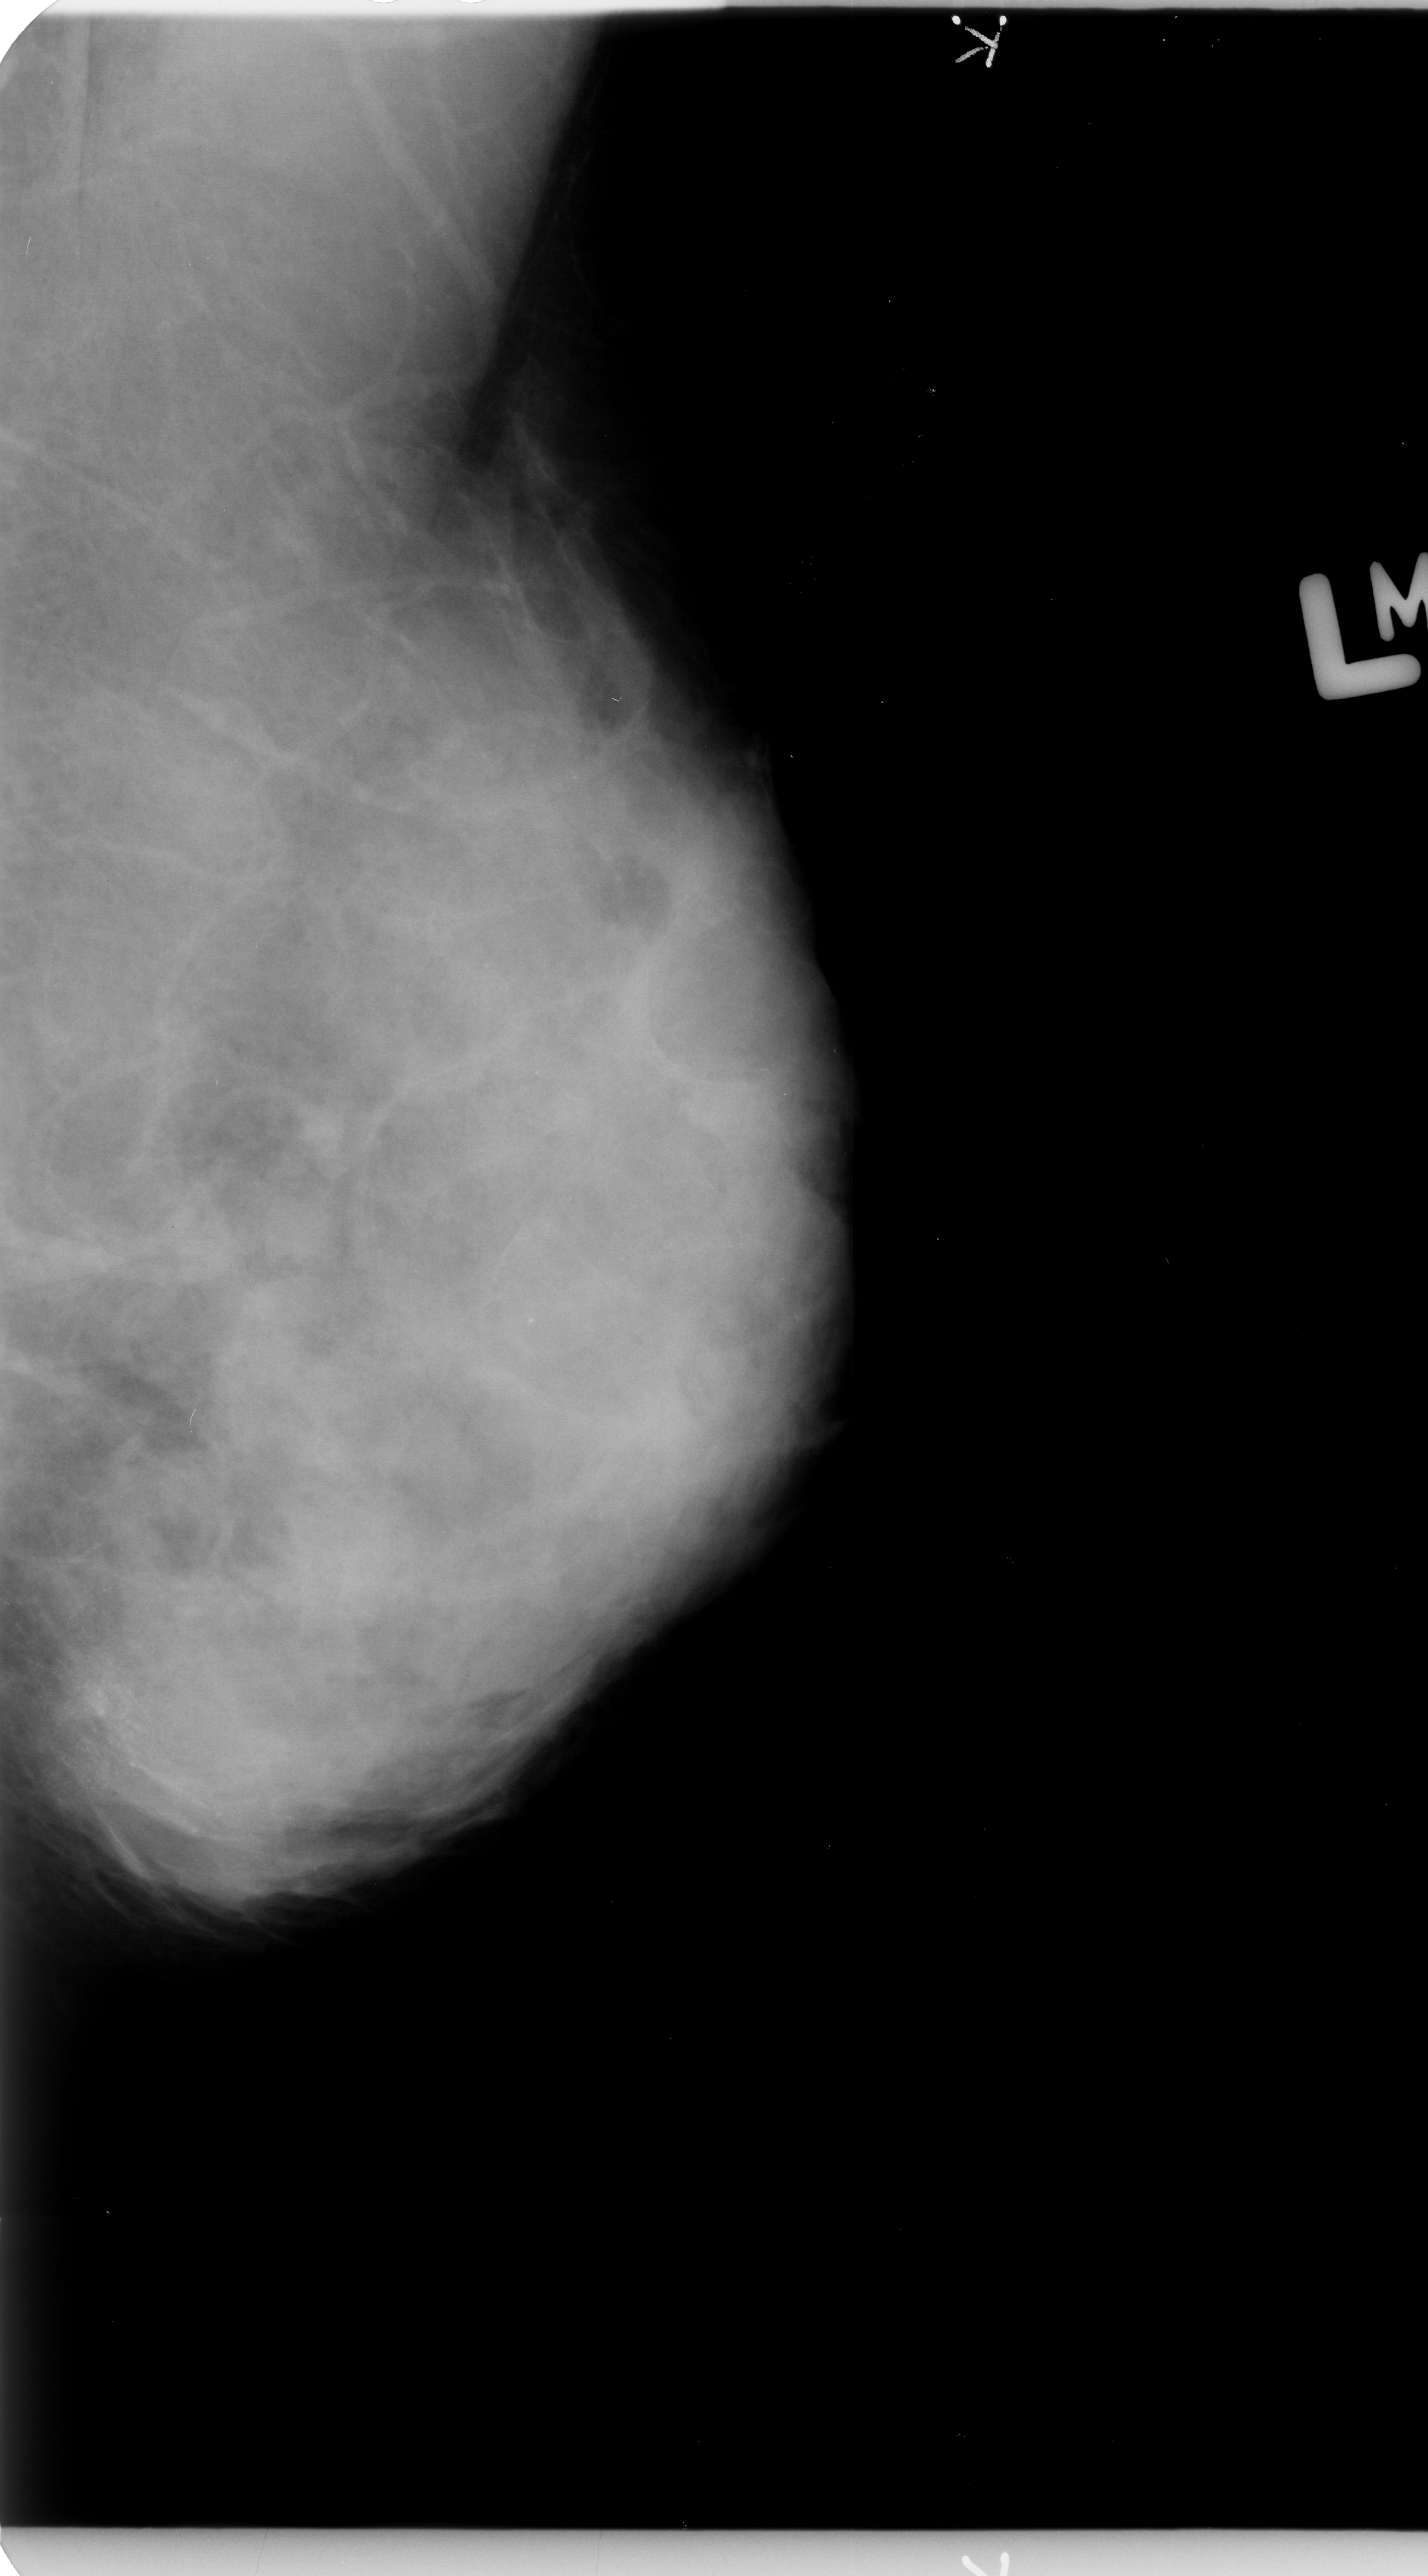
Scanned film-screen mammogram; left breast; MLO view; BI-RADS breast density category 4 (scale 1–4).
Finding: calcifications, morphology pleomorphic, distribution clustered; BI-RADS assessment category 4; pathology (as recorded): malignant.